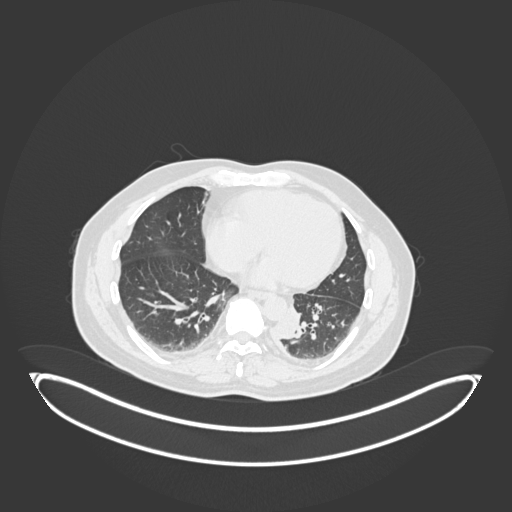
Chest CT, one axial slice; position 61 of 258 along the scan axis; reconstruction kernel B30f; 120 kVp; lung window (W 1500 / L -600 HU); 1 mm slice thickness; 512 × 512 image matrix, field of view 500 × 500 mm. Male patient, age 54 years. From the clinical record (not read from this slice): clinical TNM (as recorded): T3 N0 M0.
Annotated regions visible in this slice (rectangle marked by the reading radiologist):
- lung tumour (recorded histology: squamous cell carcinoma): bounding box (x1, y1, x2, y2) in pixels: (274, 307, 306, 343)